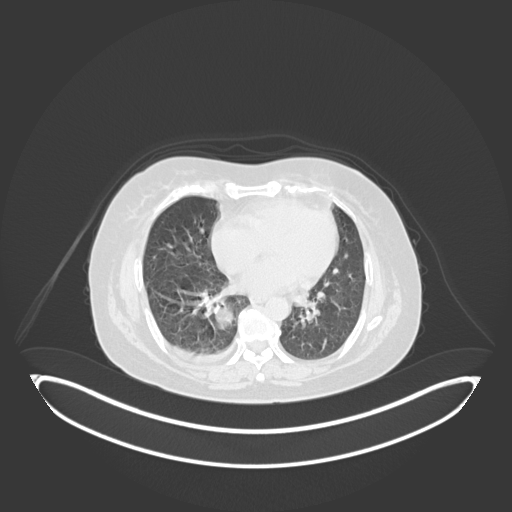
Chest CT, one axial slice. Position 63 of 231 along the scan axis. Reconstruction kernel B30f. 120 kVp. Lung window (W 1500 / L -600 HU). 512 × 512 image matrix. Female patient, age 56 years. From the clinical record (not read from this slice): clinical TNM (as recorded): T2b N1 M0; histopathological grade: G3.
Annotated regions visible in this slice (rectangle marked by the reading radiologist):
- lung tumour (recorded histology: small cell carcinoma): bounding box [x1, y1, x2, y2] px = [215, 296, 237, 336]